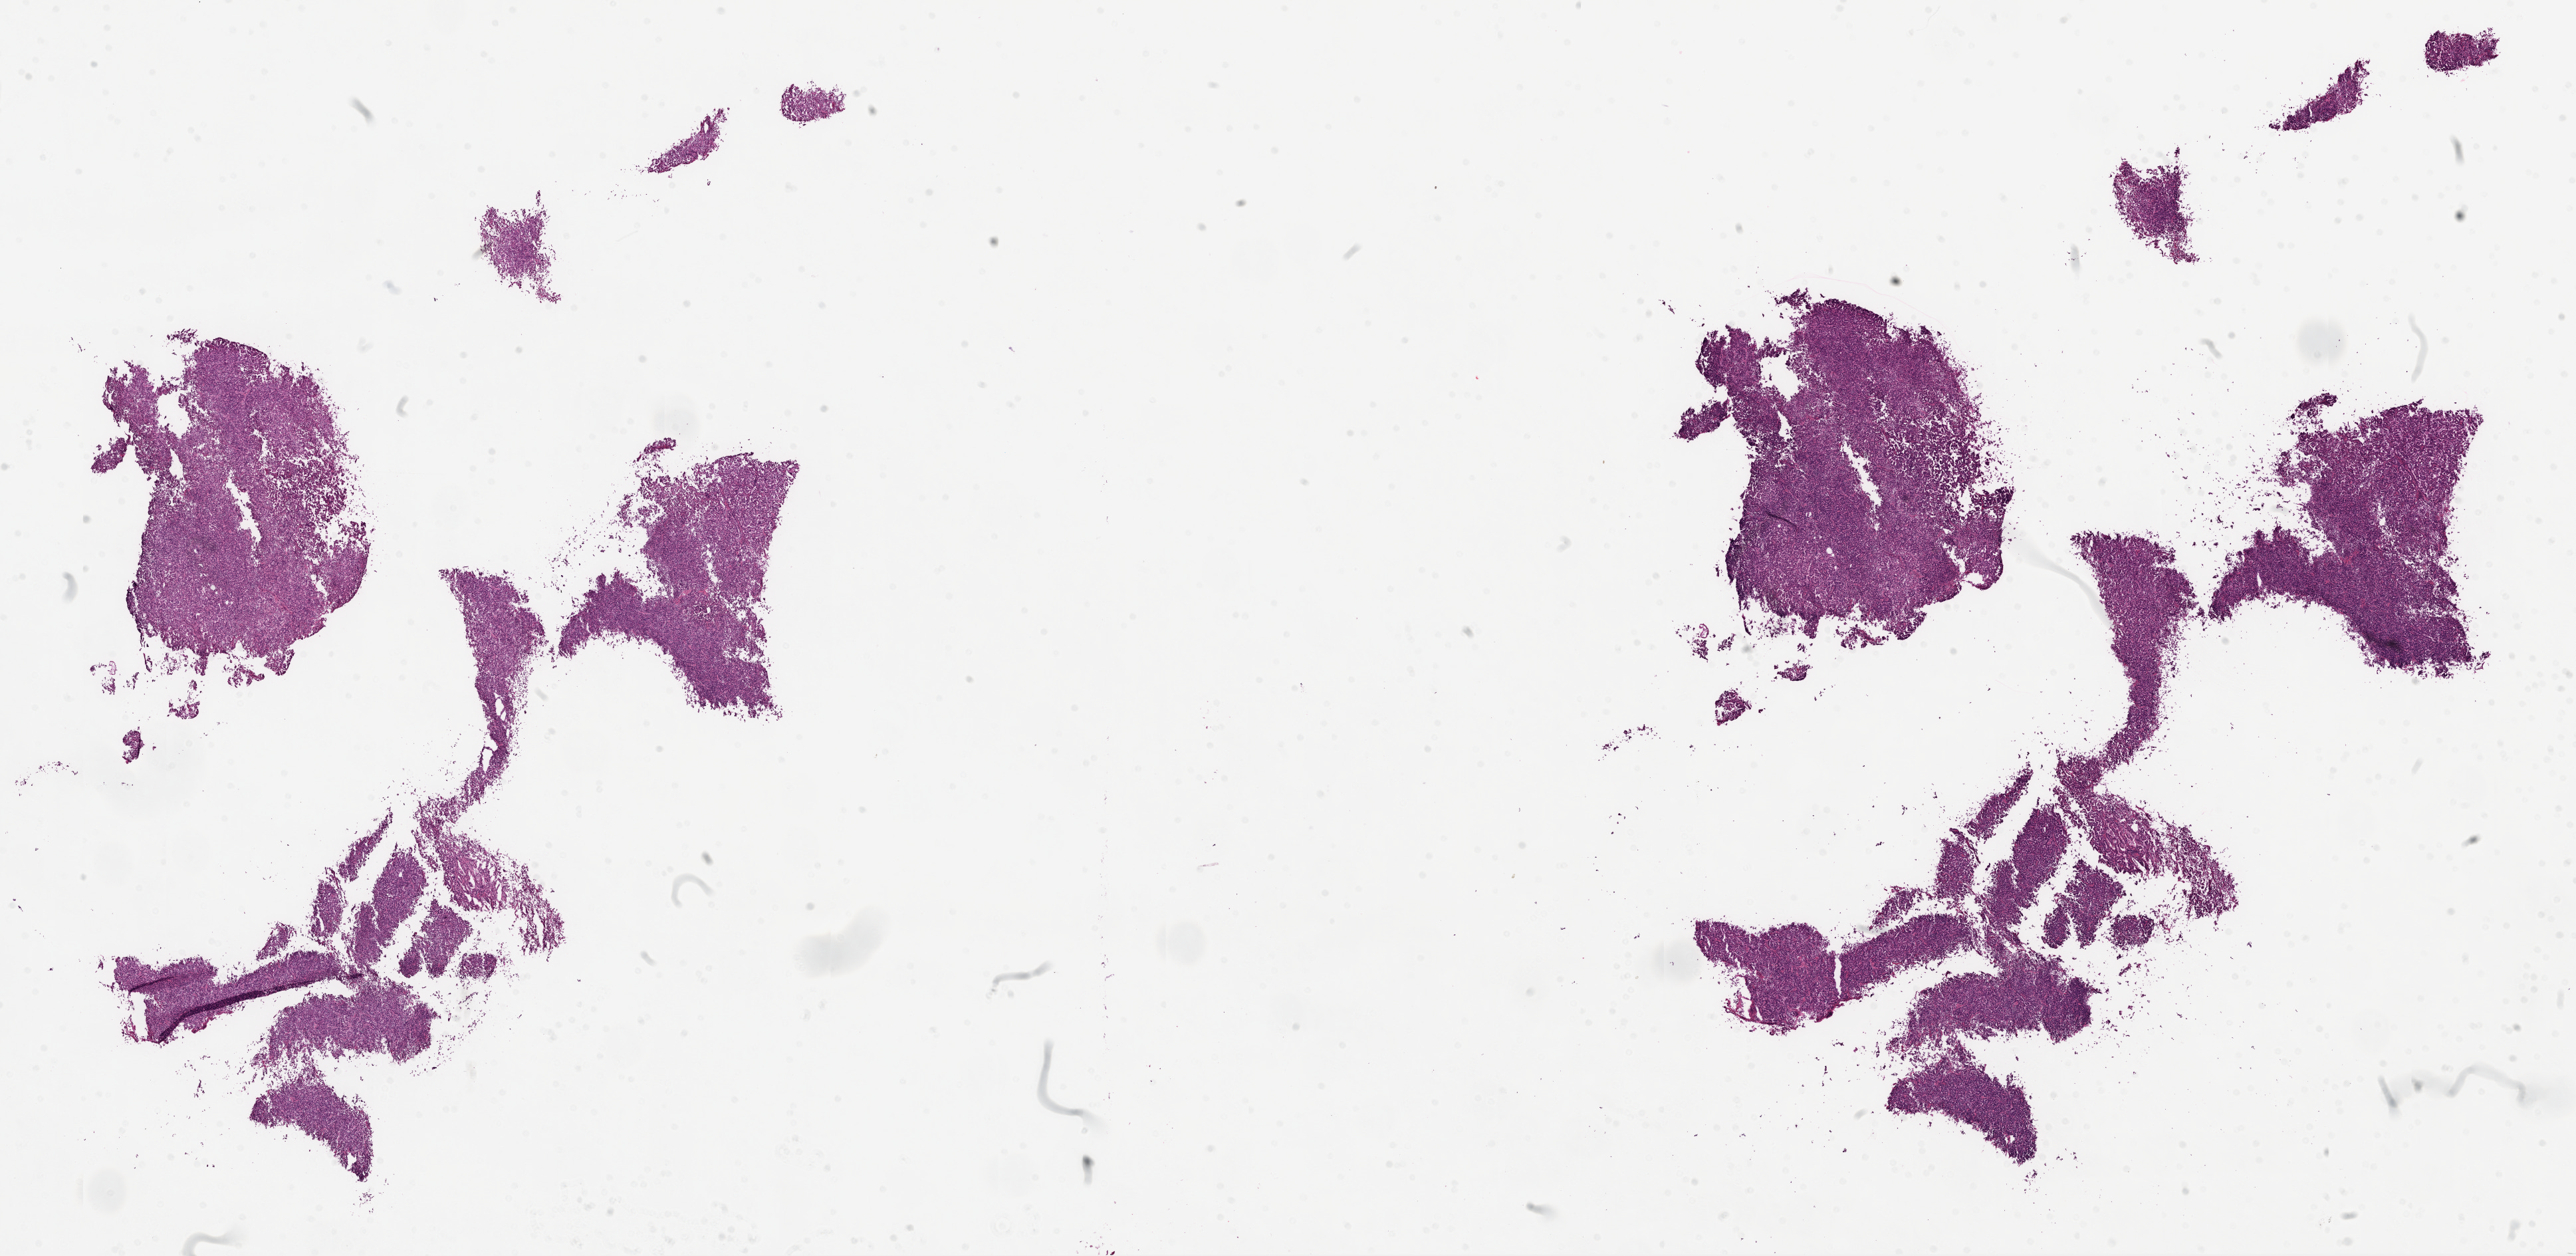
Digitized H&E-stained tissue section (whole slide), whole scanned area (about 31.1 x 15.2 mm, acquisition: 20x scan) shown as a low-resolution overview. Frozen section. Sample: primary tumour, kidney. Male patient; age at initial diagnosis 51 years.
Diagnosis: Papillary adenocarcinoma, NOS.